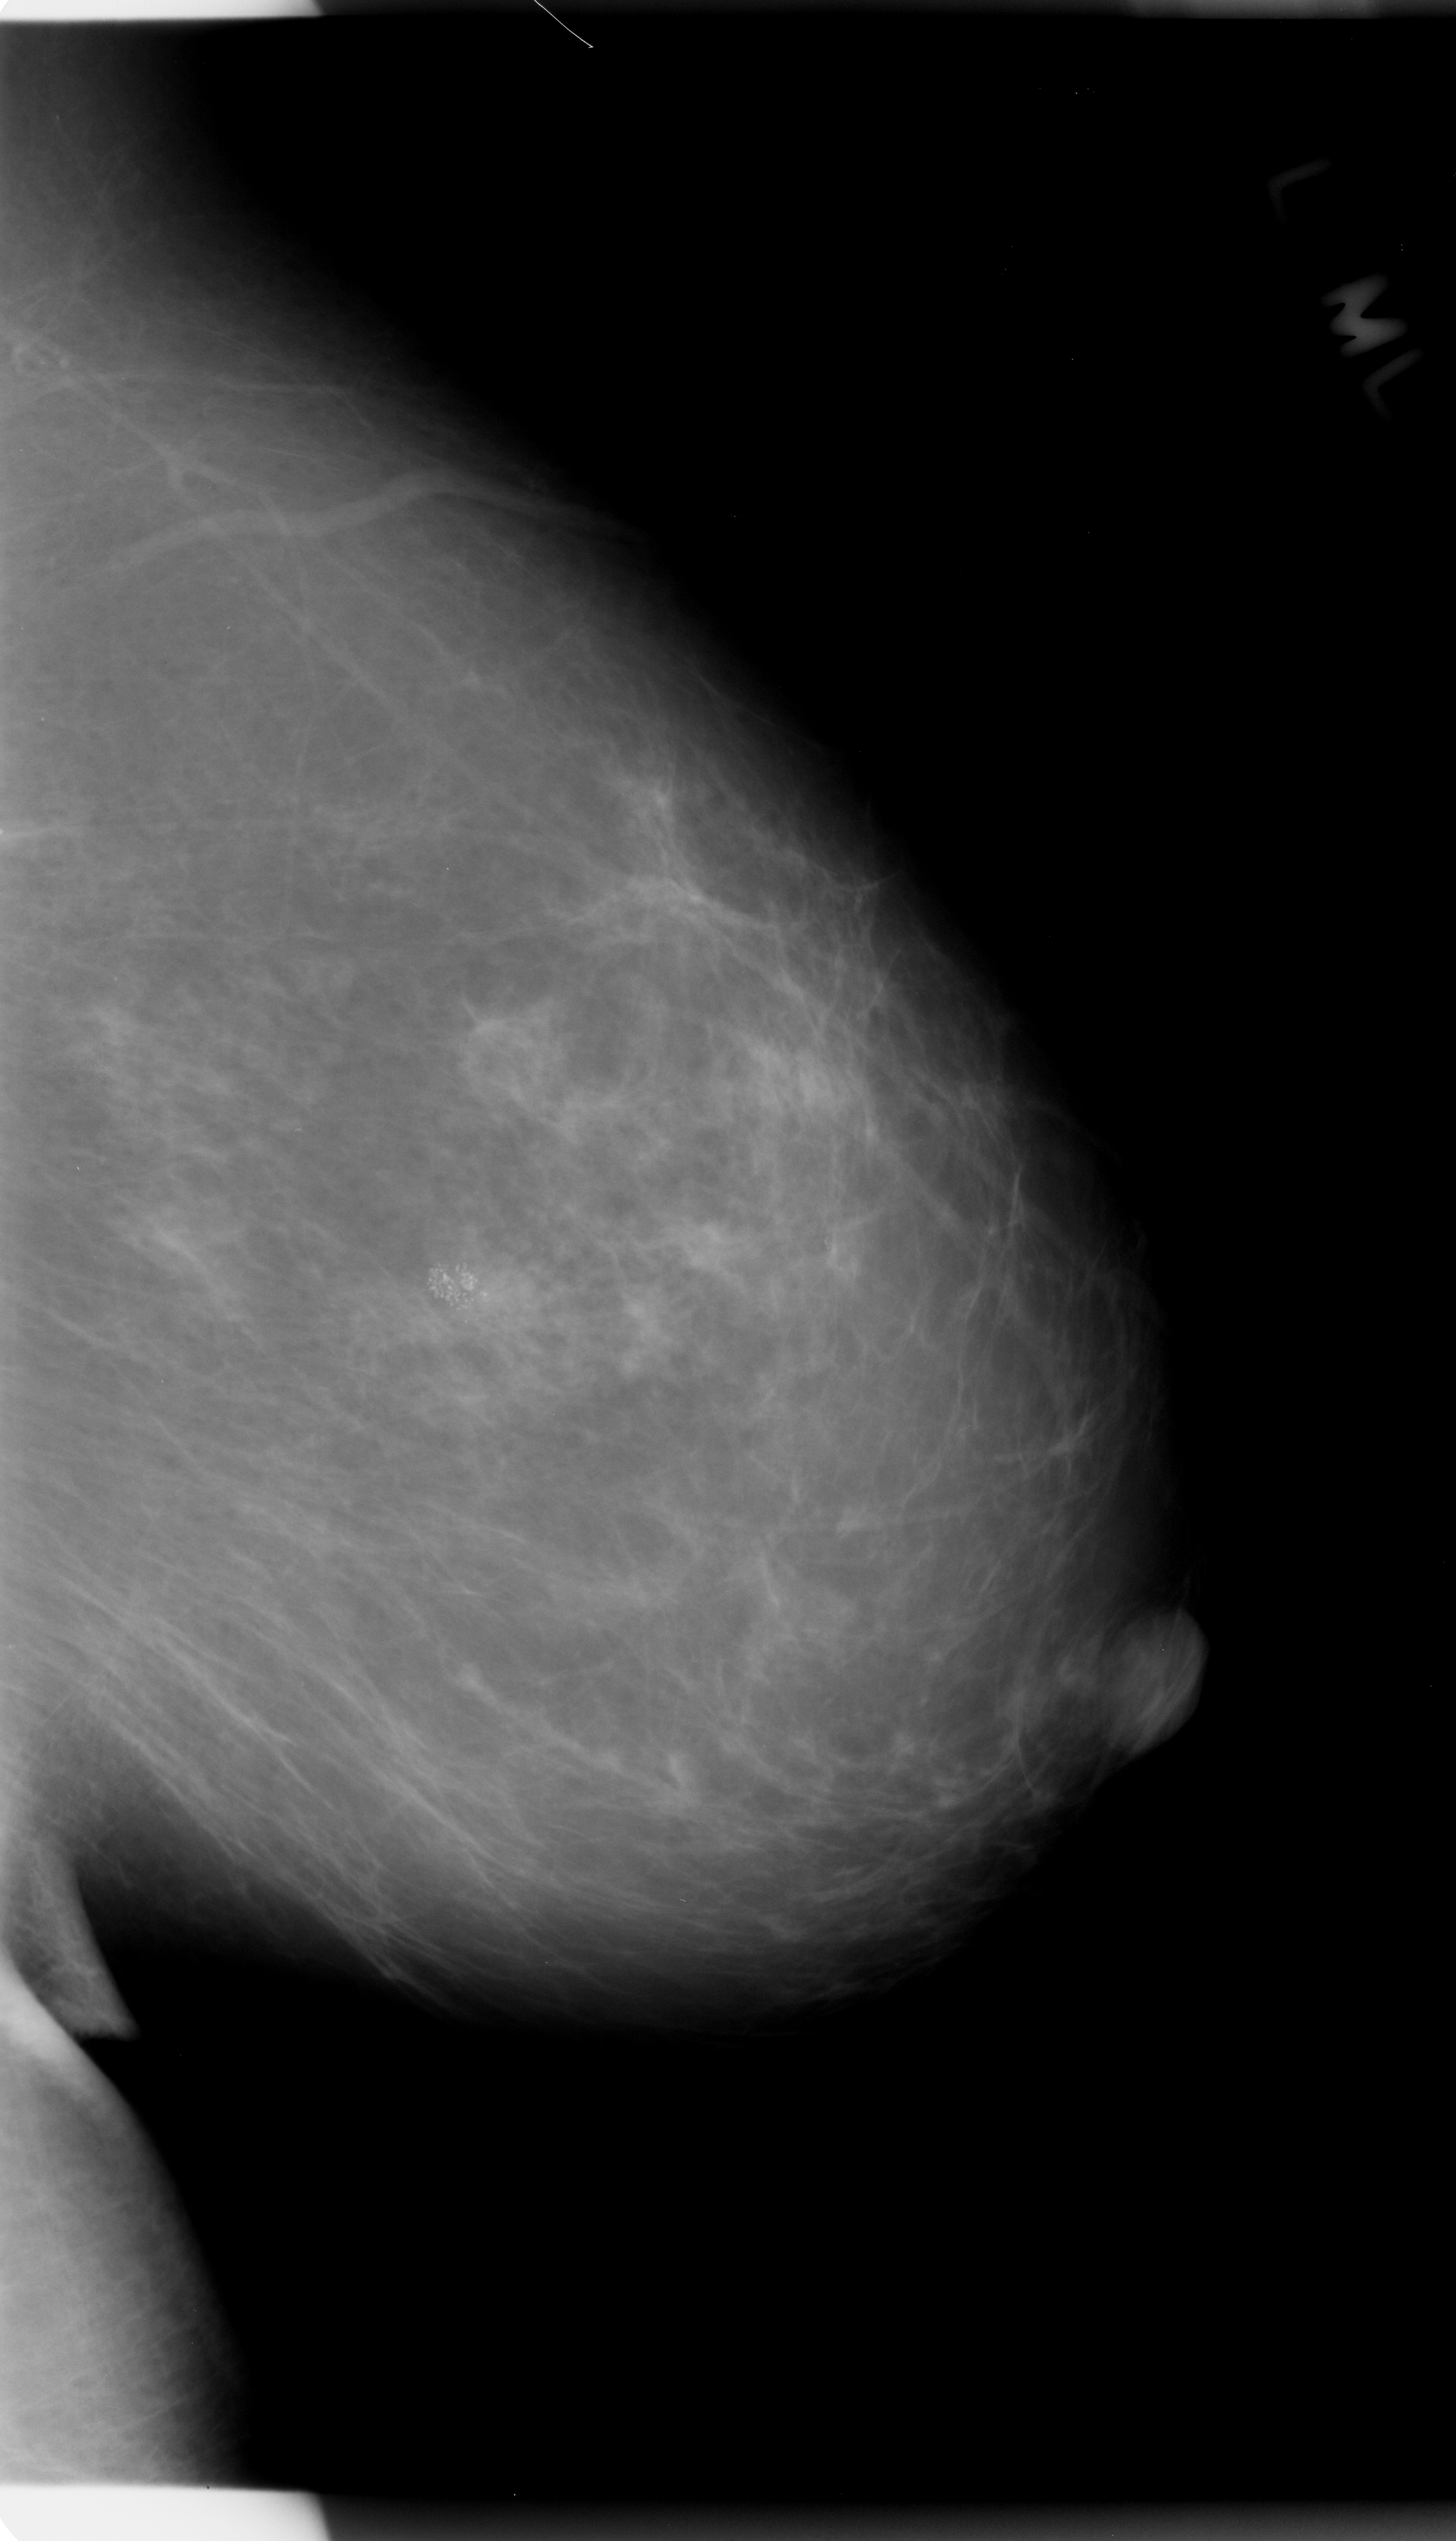
Scanned film-screen mammogram, left breast, mediolateral oblique (MLO) view, BI-RADS breast density category 2 (scale 1–4).
Marked abnormality: calcifications, morphology pleomorphic, distribution clustered; BI-RADS assessment category 4; pathology (as recorded): malignant.